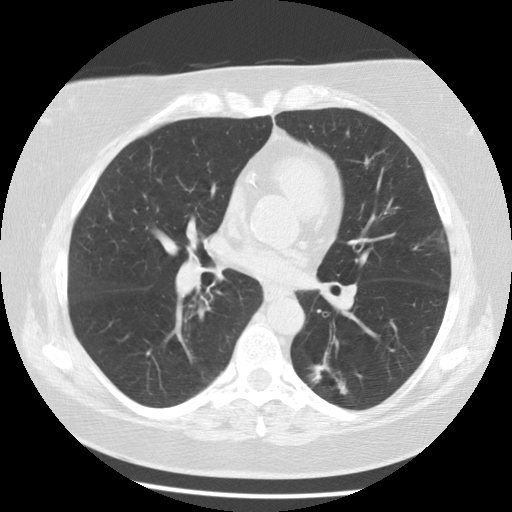
Chest CT (low-dose screening protocol), one axial image; third annual screen; lung window (W 1500 / L -600 HU); 2.5 mm slice thickness; 120 kVp; slice 58 of 116 in the series; 512 × 512 image matrix, field of view 341 × 341 mm. Female participant, aged 59 years at enrolment.
Lesion marked by an expert reader, box from (x=295, y=348) to (x=358, y=406) px. The screening reader recorded 6 non-calcified nodules or masses ≥4 mm on this exam; which of them this box marks is not recorded. Official screen result: positive, other.